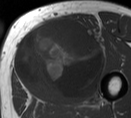
MRI of an extremity soft-tissue mass, one axial slice. Slice 37 of 55 in the series (ordered by position). MR volume resampled by the dataset authors to the PET/CT grid (not the native acquisition matrix). 3.27 mm slice thickness. 131 × 118 image matrix, field of view 128 × 115 mm. Male patient. From the clinical record (not read from this slice): histological type: pleiomorphic liposarcoma; grade: high; site of the primary tumour: left thigh.
Structures marked on this image (expert contour drawn on MRI and transferred to this co-registered scan by the dataset authors):
- gross tumour volume including surrounding oedema: box from (x=16, y=18) to (x=106, y=99) px
- gross tumour volume (mass): (x=16, y=18)–(x=104, y=99)